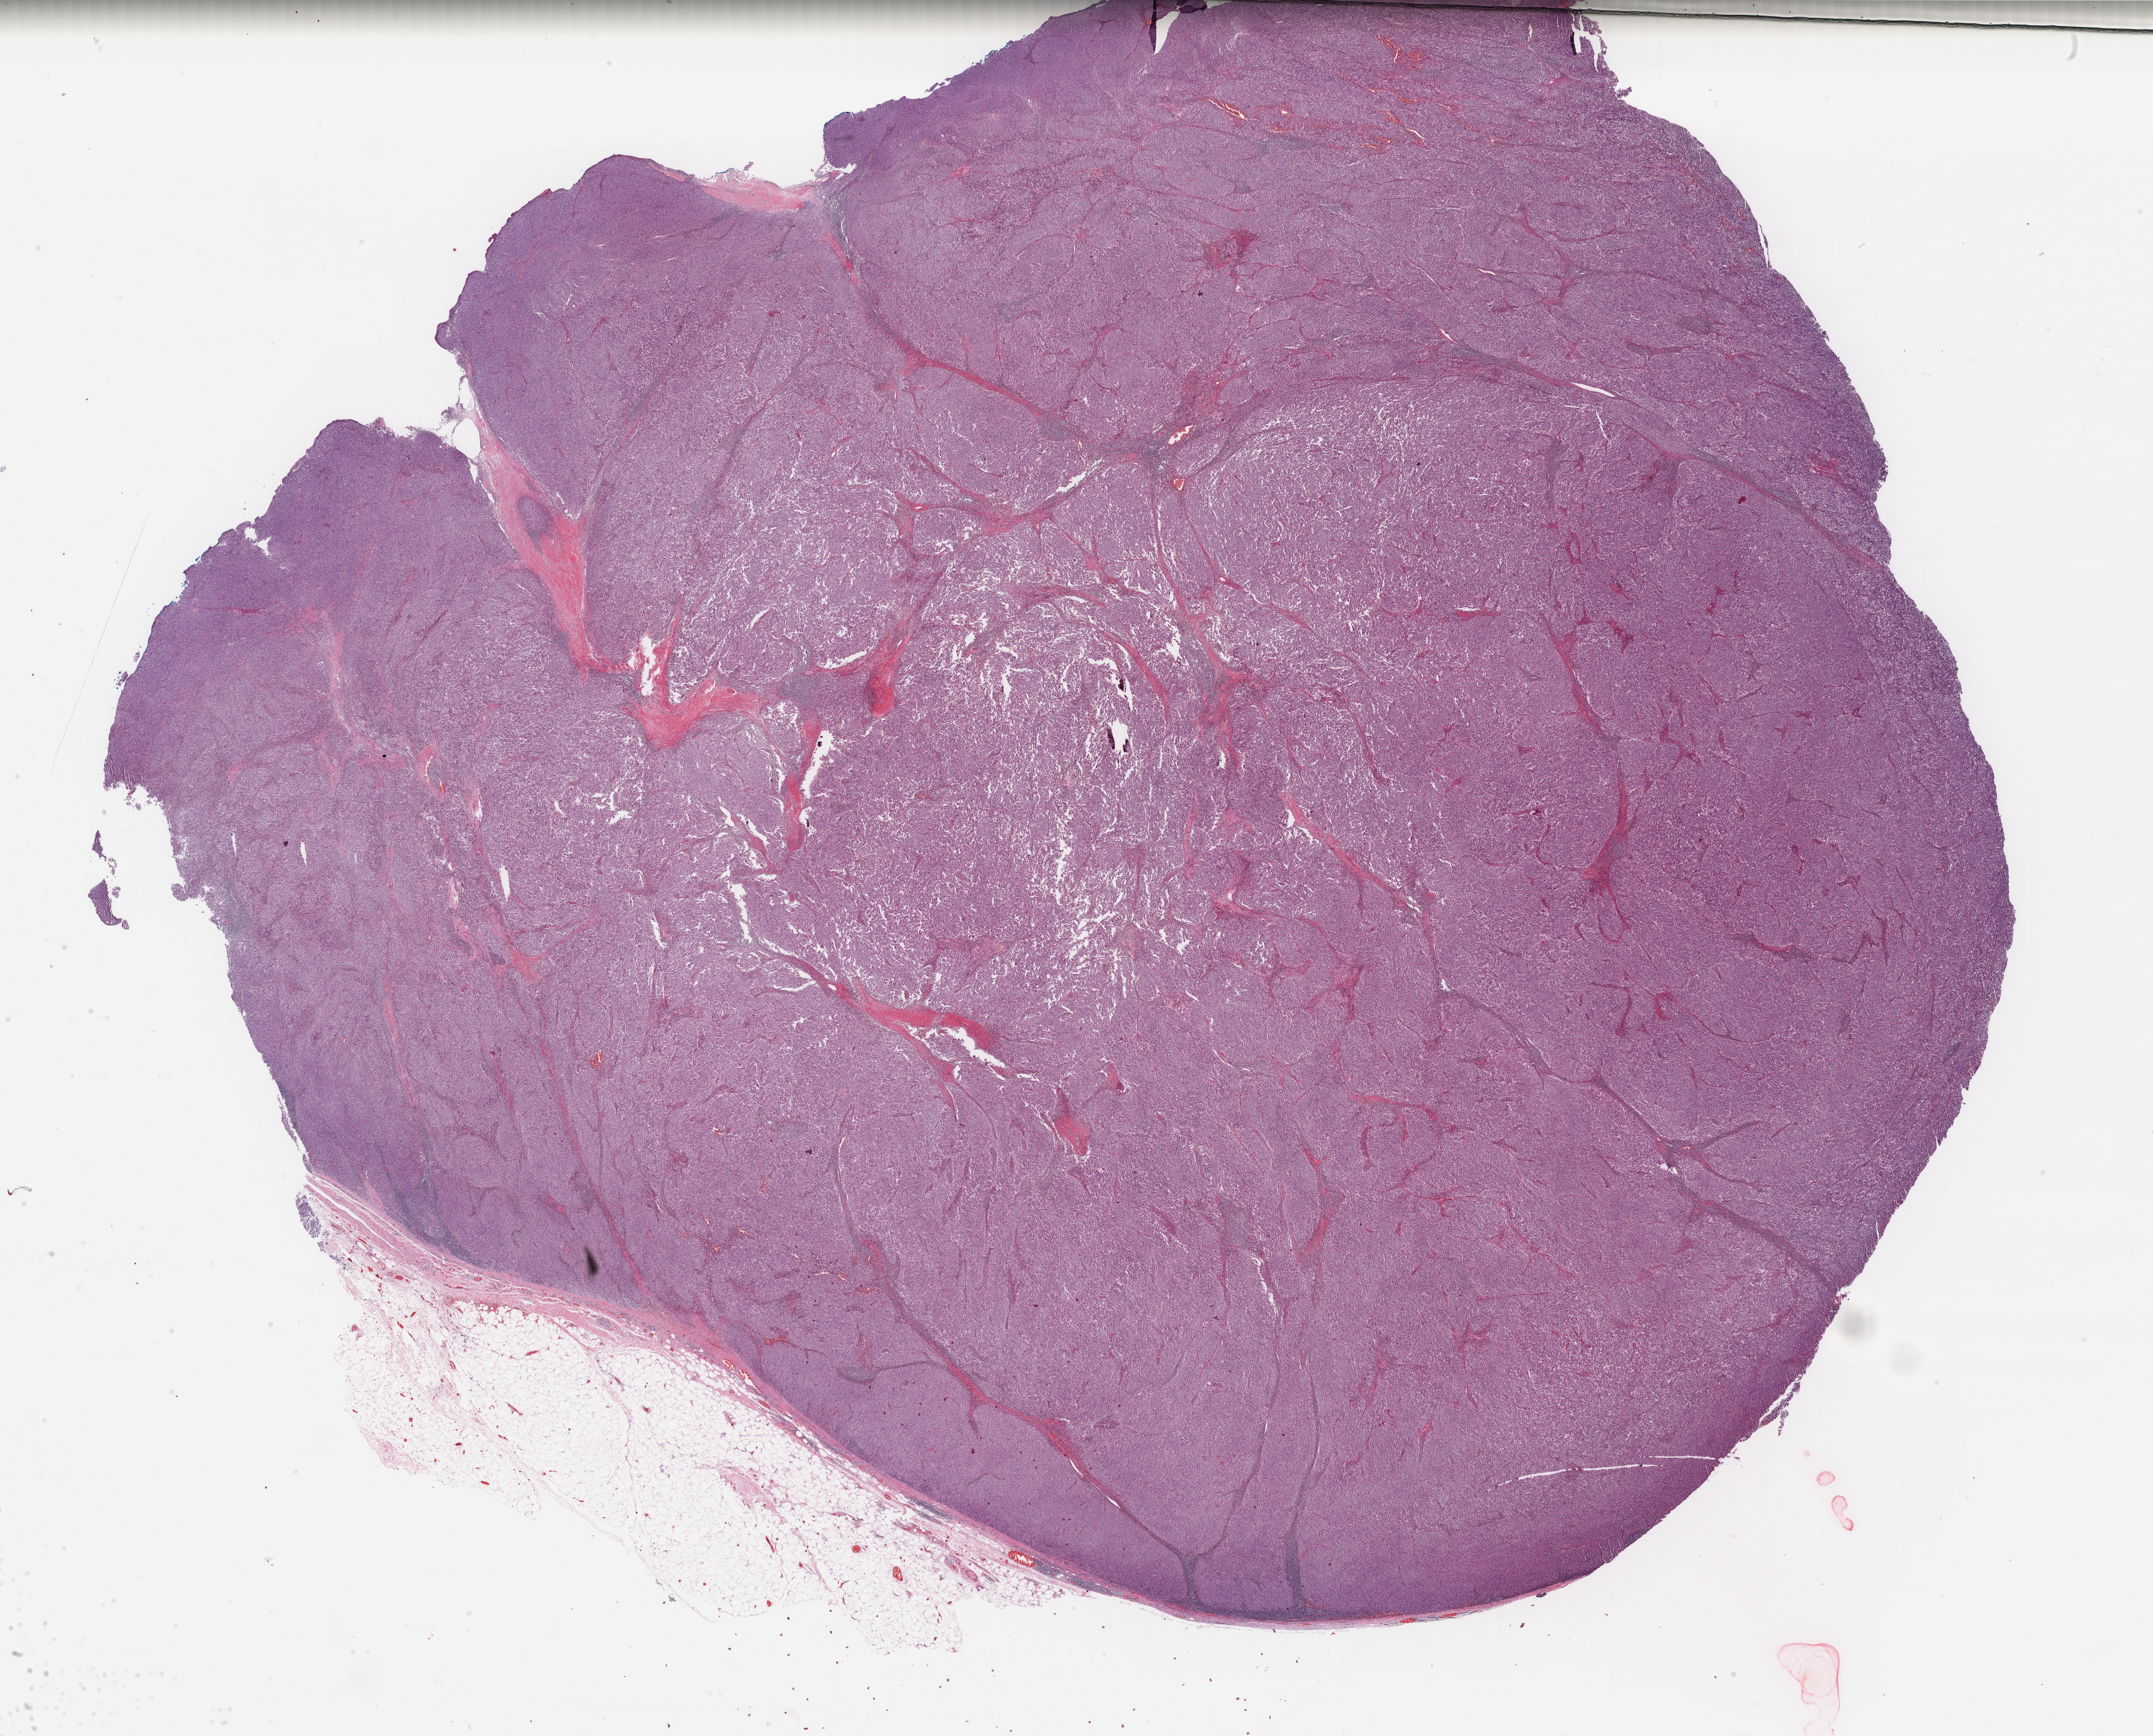
Digitized H&E-stained tissue section (whole slide) — a low-resolution overview of the entire scanned area, about 28.6 x 23.0 mm (slide scanned at 40x); FFPE section; primary tumour sample from the skin. Patient: female, age at initial diagnosis 47 years.
Histologic diagnosis: Malignant melanoma, NOS.